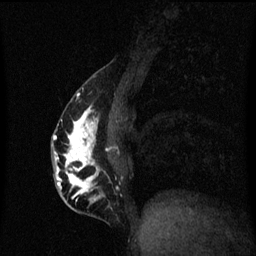
Breast MRI (dynamic contrast-enhanced), one sagittal slice. Position 24 of 60 along the scan axis. Dynamic contrast-enhanced series, image 2 of 3 at this slice position (ordered by acquisition). 1.5 T. TE 4.2 ms, TR 8.4 ms. 2 mm slice thickness. 256 × 256 image matrix, field of view 200 × 200 mm. Patient: female, 40 years.
Structures marked on this image (semi-automatically segmented with operator editing):
- analysis volume of interest (the breast-tissue region the enhancement analysis was run in; not a lesion): bounding box <52,84,117,211> (left, top, right, bottom; pixels)
- tumour enhancement mask (voxels above the 70 % enhancement threshold inside the analysis volume of interest): <54,106,101,203>